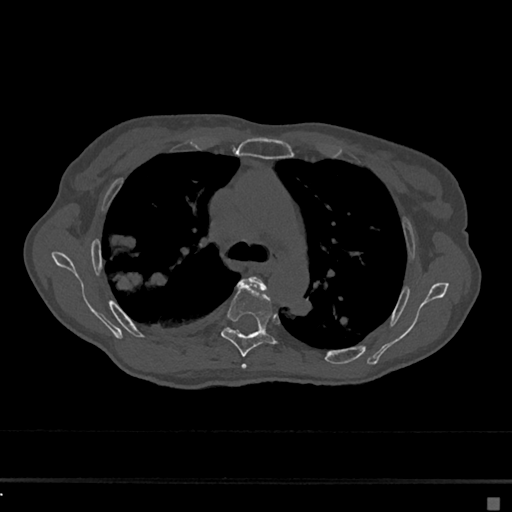
CT including the spine, one axial slice. Slice 463 of 797 in the series (ordered by position). 120 kVp. Bone window (W 1800 / L 400 HU). 0.5 mm slice thickness. 512 × 512 image matrix, field of view 360 × 360 mm. Female patient, age 68 years. Case-level facts recorded for this patient, not image findings: primary cancer: renal.
Structures marked on this image (semi-automatic segmentation, software-assisted and operator-edited):
- T4 vertebra: bounding box <241,276,268,370> (left, top, right, bottom; pixels)
- T5 vertebra: <220,280,277,357>